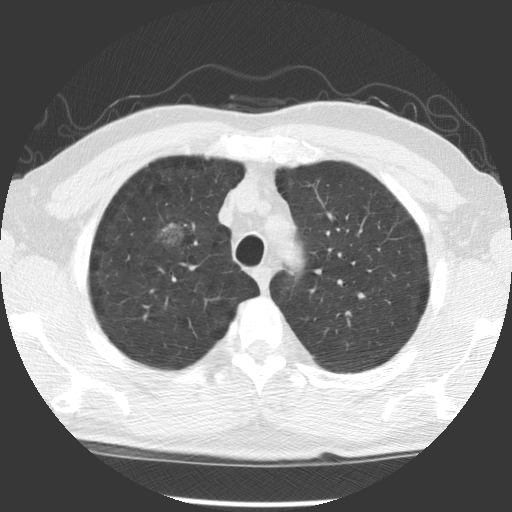
Low-dose screening chest CT, axial slice; baseline annual screen; lung window (W 1500 / L -600 HU); 2.5 mm slice thickness; slice 91 of 122 in the series; 512 × 512 image matrix. Male participant, aged 60 years at enrolment. Former smoker at enrolment.
• Expert reader's lesion annotation, bounding box [x1, y1, x2, y2] px = [141, 211, 203, 262].
• The exam's reader record, not a measurement of the box and not confirmed to be the same lesion: non-calcified nodule or mass ≥4 mm, right middle lobe, 20 × 20 mm, poorly defined margins, ground glass attenuation.
• Official screen result: positive, change unspecified: nodule(s) >= 4 mm or enlarging nodule(s), mass(es), or other non-specific abnormalities suspicious for lung cancer.
• Later outcome: lung cancer diagnosed 863 days after this screen — papillary adenocarcinoma, NOS, right upper lobe, moderately differentiated (G2), stage IB (AJCC 6th edition), 32 mm at pathology.